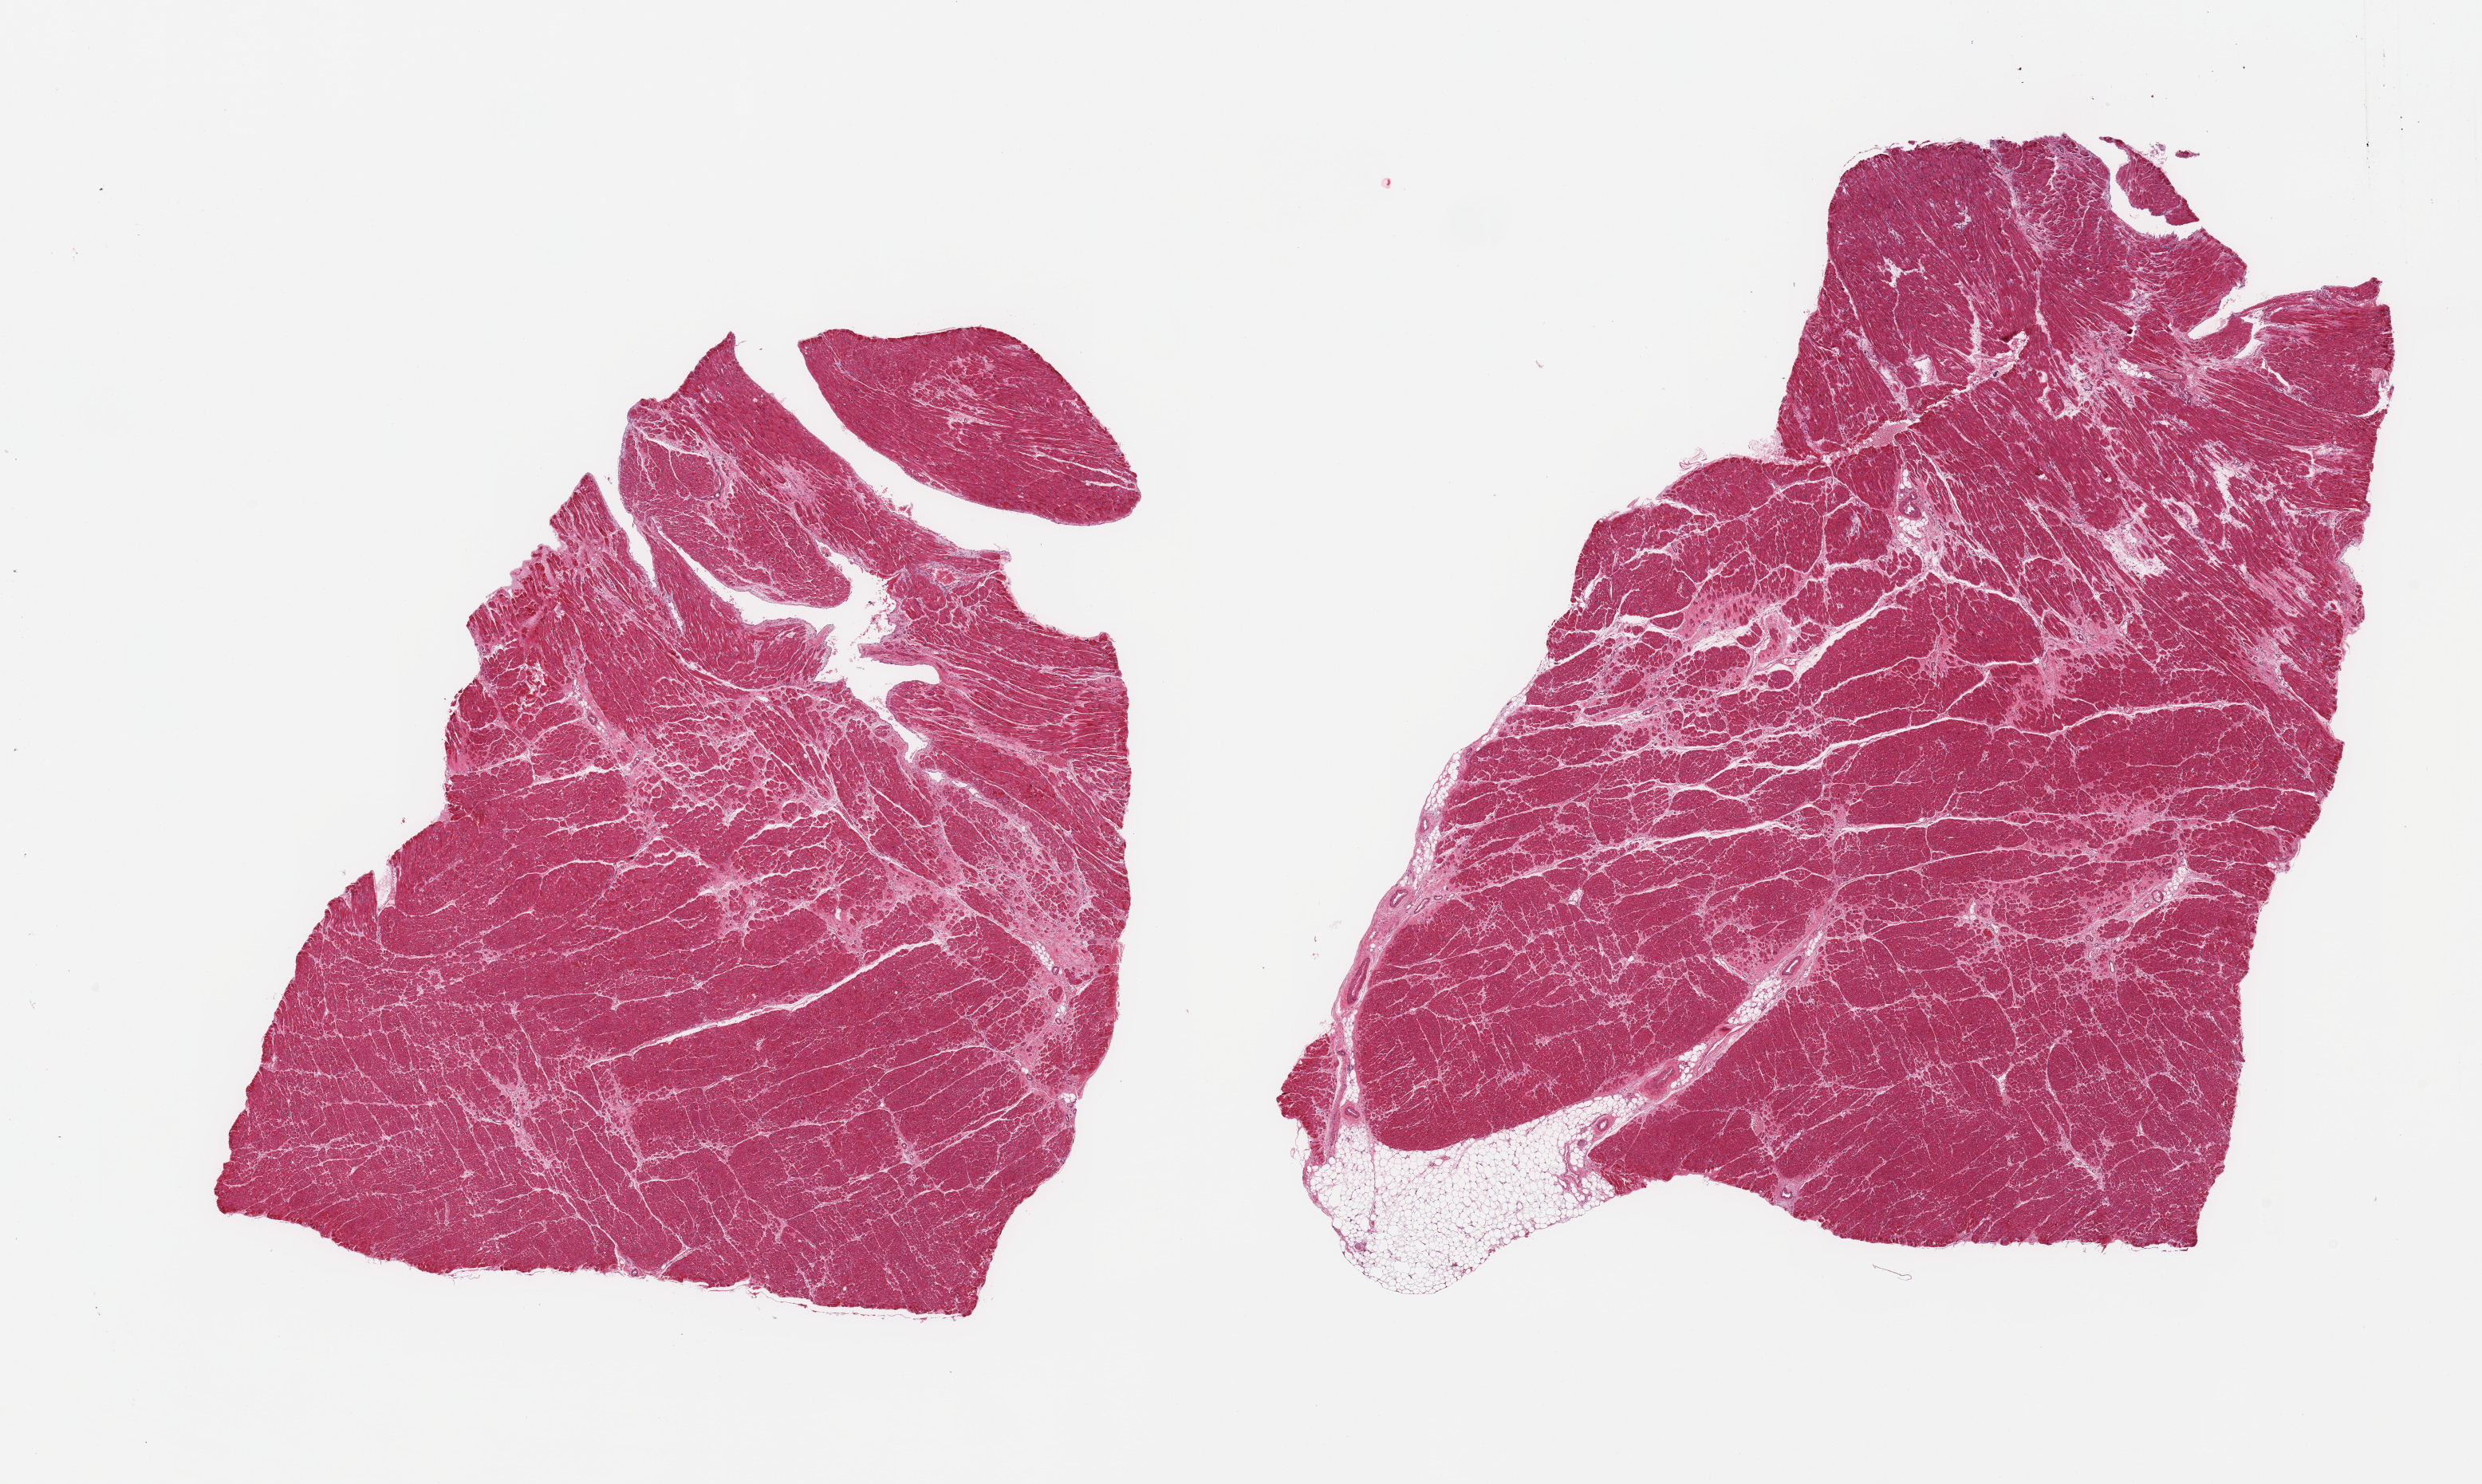
Whole-slide image, haematoxylin and eosin stain, brightfield, a low-resolution overview of the entire scanned area, about 24.6 x 14.7 mm (slide scanned at 20x), PAXgene-fixed, paraffin-embedded tissue, sampled site (target tissue): heart, tissue donor sample. Donor: female.
Reviewer comment on this tissue sample: 2 pieces; patchy myocardial scarring comprising 5%.